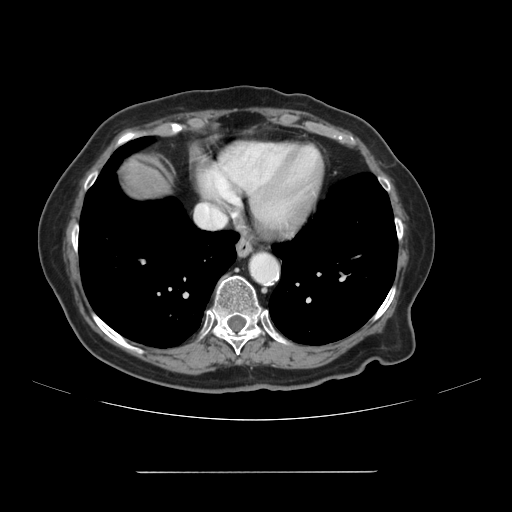
Contrast-enhanced abdominal CT, one axial slice; position 108 of 111 along the scan axis; intravenous contrast given; soft-tissue window (W 400 / L 40 HU); 2.5 mm slice thickness; 512 × 512 image matrix, field of view 400 × 400 mm. Female patient, age 74 years. Case-level facts recorded for this patient, not image findings: diagnosis: colorectal cancer liver metastases, imaged before liver resection.
Outlined on this slice (outlined manually by an expert reader):
- liver: bounding box (x1, y1, x2, y2) in pixels: (118, 156, 171, 201)